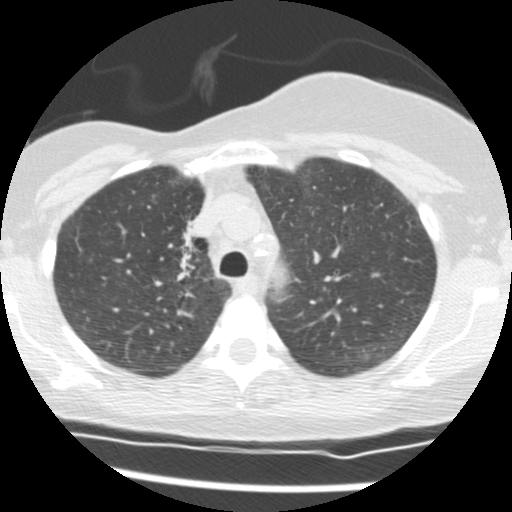
Chest CT (low-dose screening protocol), one axial image, second annual screen, lung window (W 1500 / L -600 HU), 2.5 mm slice thickness, standard (soft-tissue) reconstruction kernel (STANDARD), slice 32 of 165 in the series. Female, age 56 years at enrolment. Current smoker at enrolment.
• Expert reader's lesion annotation, bounding box <155,213,215,284> (left, top, right, bottom; pixels).
• The screening reader recorded 2 non-calcified nodules or masses ≥4 mm on this exam (right middle lobe, right lower lobe); which of them this box marks is not recorded.
• Official screen result: positive, change unspecified: nodule(s) >= 4 mm or enlarging nodule(s), mass(es), or other non-specific abnormalities suspicious for lung cancer.
• Lung cancer was diagnosed 675 days after this screen: adenocarcinoma, NOS, right upper lobe, stage IIIB (AJCC 6th edition), 8 mm at pathology.